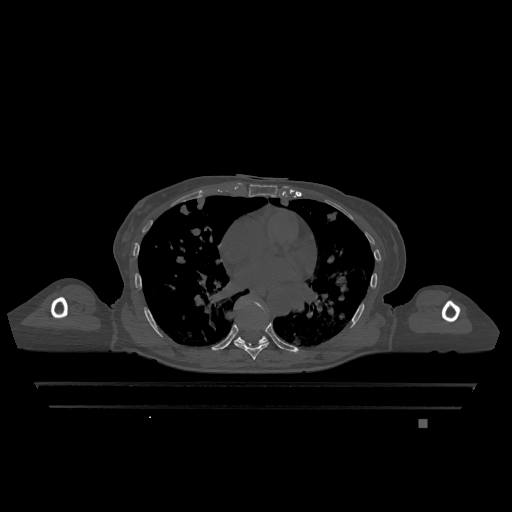
CT including the spine, one axial slice; position 721 of 1317 along the scan axis; bone window (W 1800 / L 400 HU); 512 × 512 image matrix. Female patient, age 74 years. From the clinical record (not read from this slice): primary cancer: lung.
Structures marked on this image (semi-automatically segmented with operator editing):
- T7 vertebra: bounding box <235,325,269,360> (left, top, right, bottom; pixels)
- T9 vertebra: <234,301,268,345>